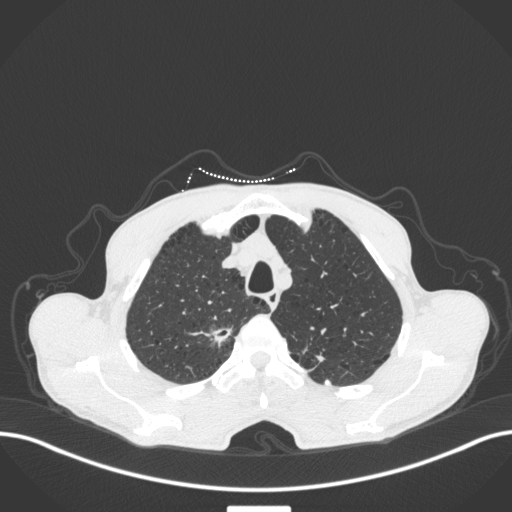
Chest CT, one axial slice; slice 354 of 445 in the series (ordered by position); reconstruction kernel B31f; 120 kVp; lung window (W 1500 / L -600 HU); 512 × 512 image matrix. Patient: male, 70 years. Case-level facts recorded for this patient, not image findings: clinical TNM (as recorded): T1a N0 M0.
Structures marked on this image (bounding box drawn by a radiologist):
- lung tumour (recorded histology: adenocarcinoma): bounding box (x1, y1, x2, y2) in pixels: (205, 321, 238, 352)